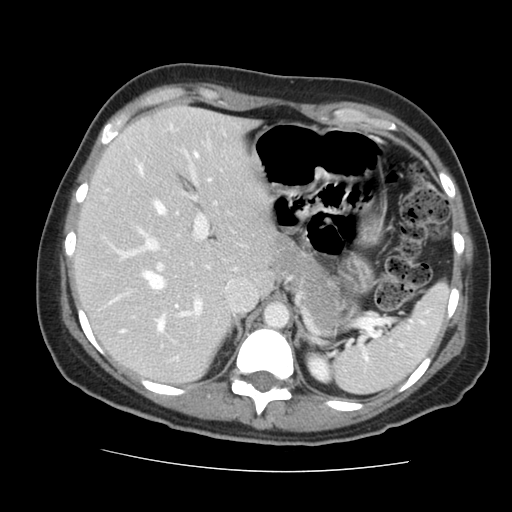
Contrast-enhanced abdominal CT, one axial slice; slice 103 of 144 in the series (ordered by position); 120 kVp; soft-tissue window (W 400 / L 40 HU); 2.5 mm slice thickness; 512 × 512 image matrix, field of view 333 × 333 mm. Female patient, age 46 years. From the clinical record (not read from this slice): diagnosis: colorectal cancer liver metastases, imaged before liver resection; multiple liver metastases: no; largest metastasis: 2.8 cm; chemotherapy before resection: yes.
Outlined on this slice (expert manual segmentation):
- hepatic veins: box from (x=138, y=164) to (x=164, y=289) px
- liver: (x=78, y=107)–(x=273, y=382)
- planned liver remnant (the part of the liver to remain after resection): (x=78, y=107)–(x=273, y=382)
- portal vein (with intrahepatic branches): (x=111, y=165)–(x=208, y=333)